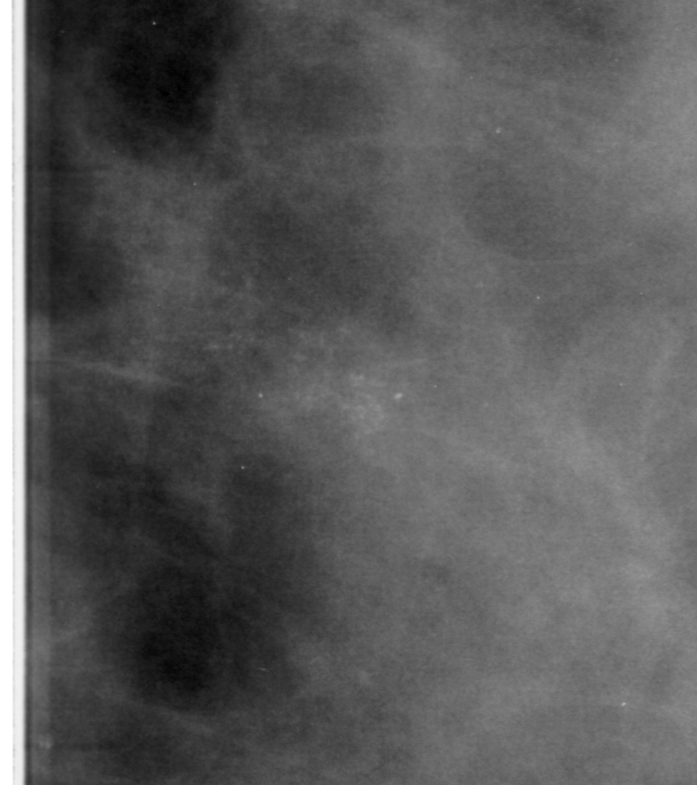
Crop from a digitized film mammogram around one marked abnormality, left breast, MLO view, BI-RADS breast density category 3 (scale 1–4).
- Marked abnormality: calcifications, morphology fine linear branching, distribution linear; BI-RADS assessment category 3; subtlety rating 3 on a 1 (subtle) to 5 (obvious) scale; pathology result (as recorded, not read from the image): malignant.